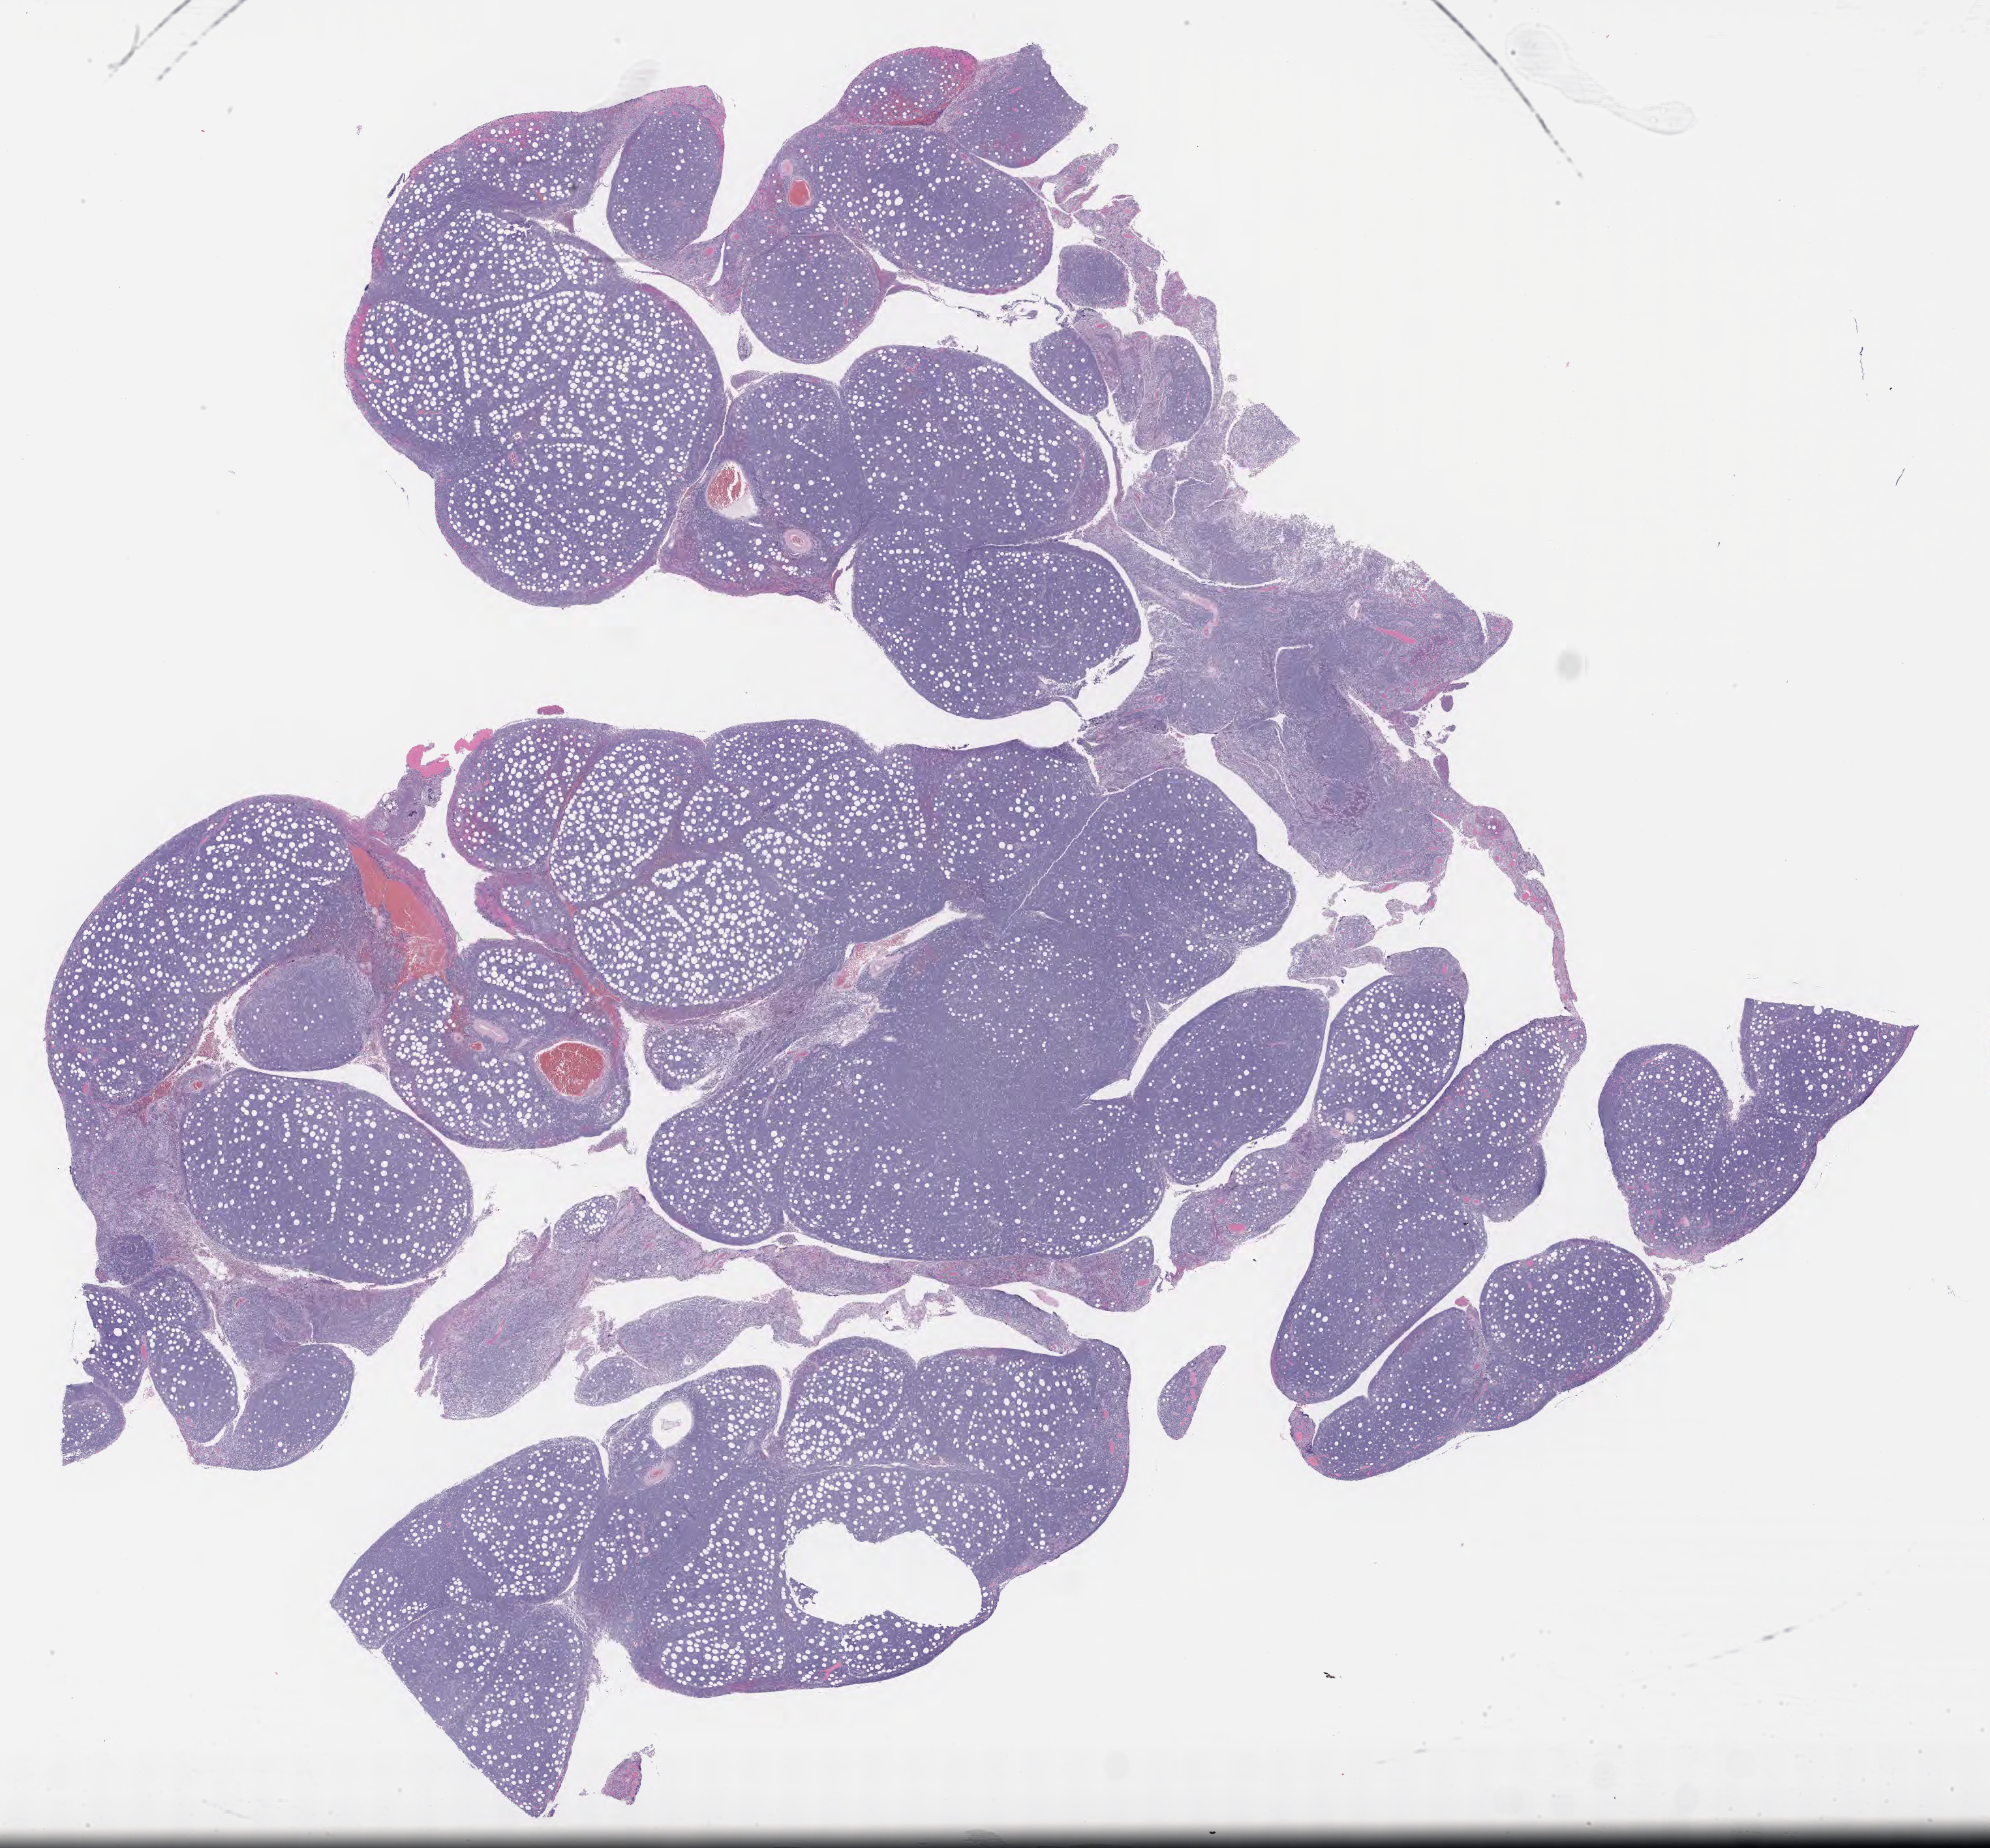
Hematoxylin and eosin (H&E) whole-slide image, shown as a low-resolution overview of the whole scanned area (about 24.7 x 22.9 mm); tumor tissue; anatomic site: small intestine. Patient male; aged 29.
Diagnosis: Burkitt lymphoma, NOS.